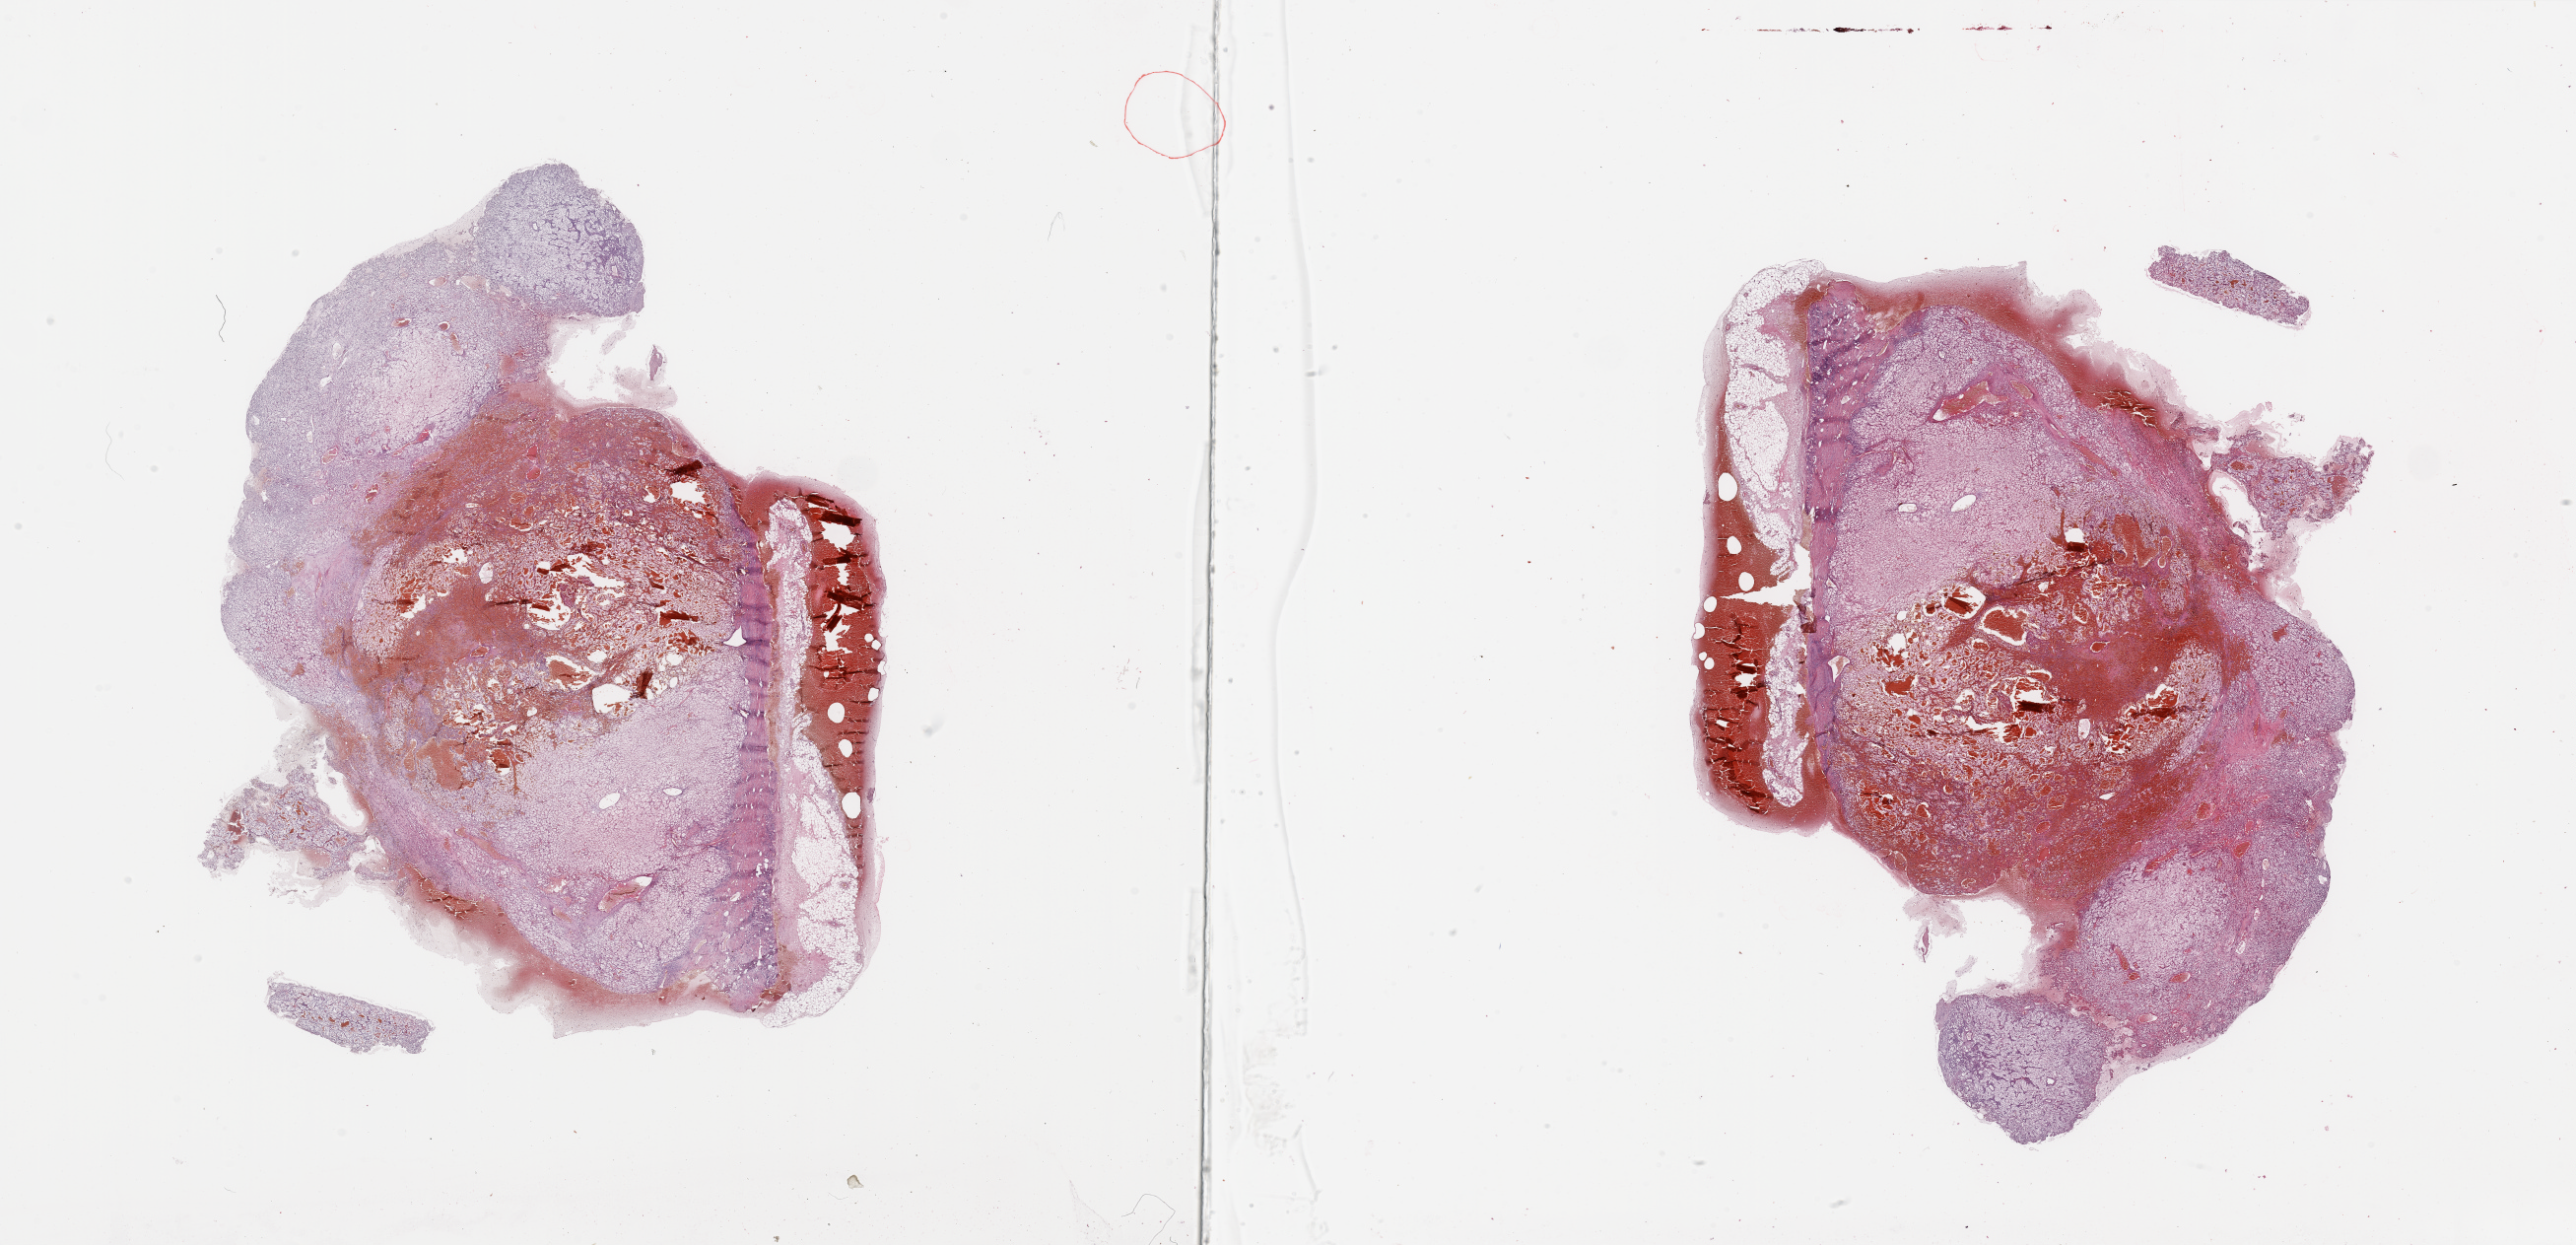
Digitized H&E-stained tissue section (whole slide) — shown as a low-resolution overview of the whole scanned area (about 41.3 x 20.0 mm). Kidney, tumour tissue. Patient: male, age 53 years. Histologic grade: G3 (poorly differentiated).
- primary tumour site (as recorded): upper pole
- diagnosis: Renal cell carcinoma, NOS
- AJCC pathologic stage: IV